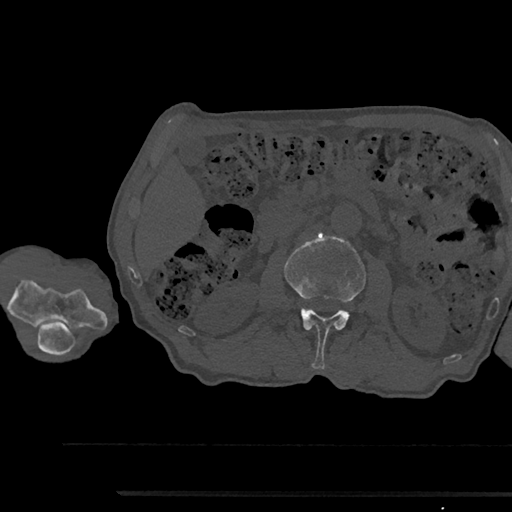
CT including the spine, one axial slice. Position 556 of 797 along the scan axis. Reconstruction kernel Br40s/3. Bone window (W 1800 / L 400 HU). 0.5 mm slice thickness. 512 × 512 image matrix, field of view 367 × 367 mm. Patient: male, 79 years. Case-level facts recorded for this patient, not image findings: primary cancer: prostate.
Outlined on this slice (semi-automatically segmented with operator editing):
- L2 vertebra: bounding box [x1, y1, x2, y2] px = [285, 233, 366, 369]